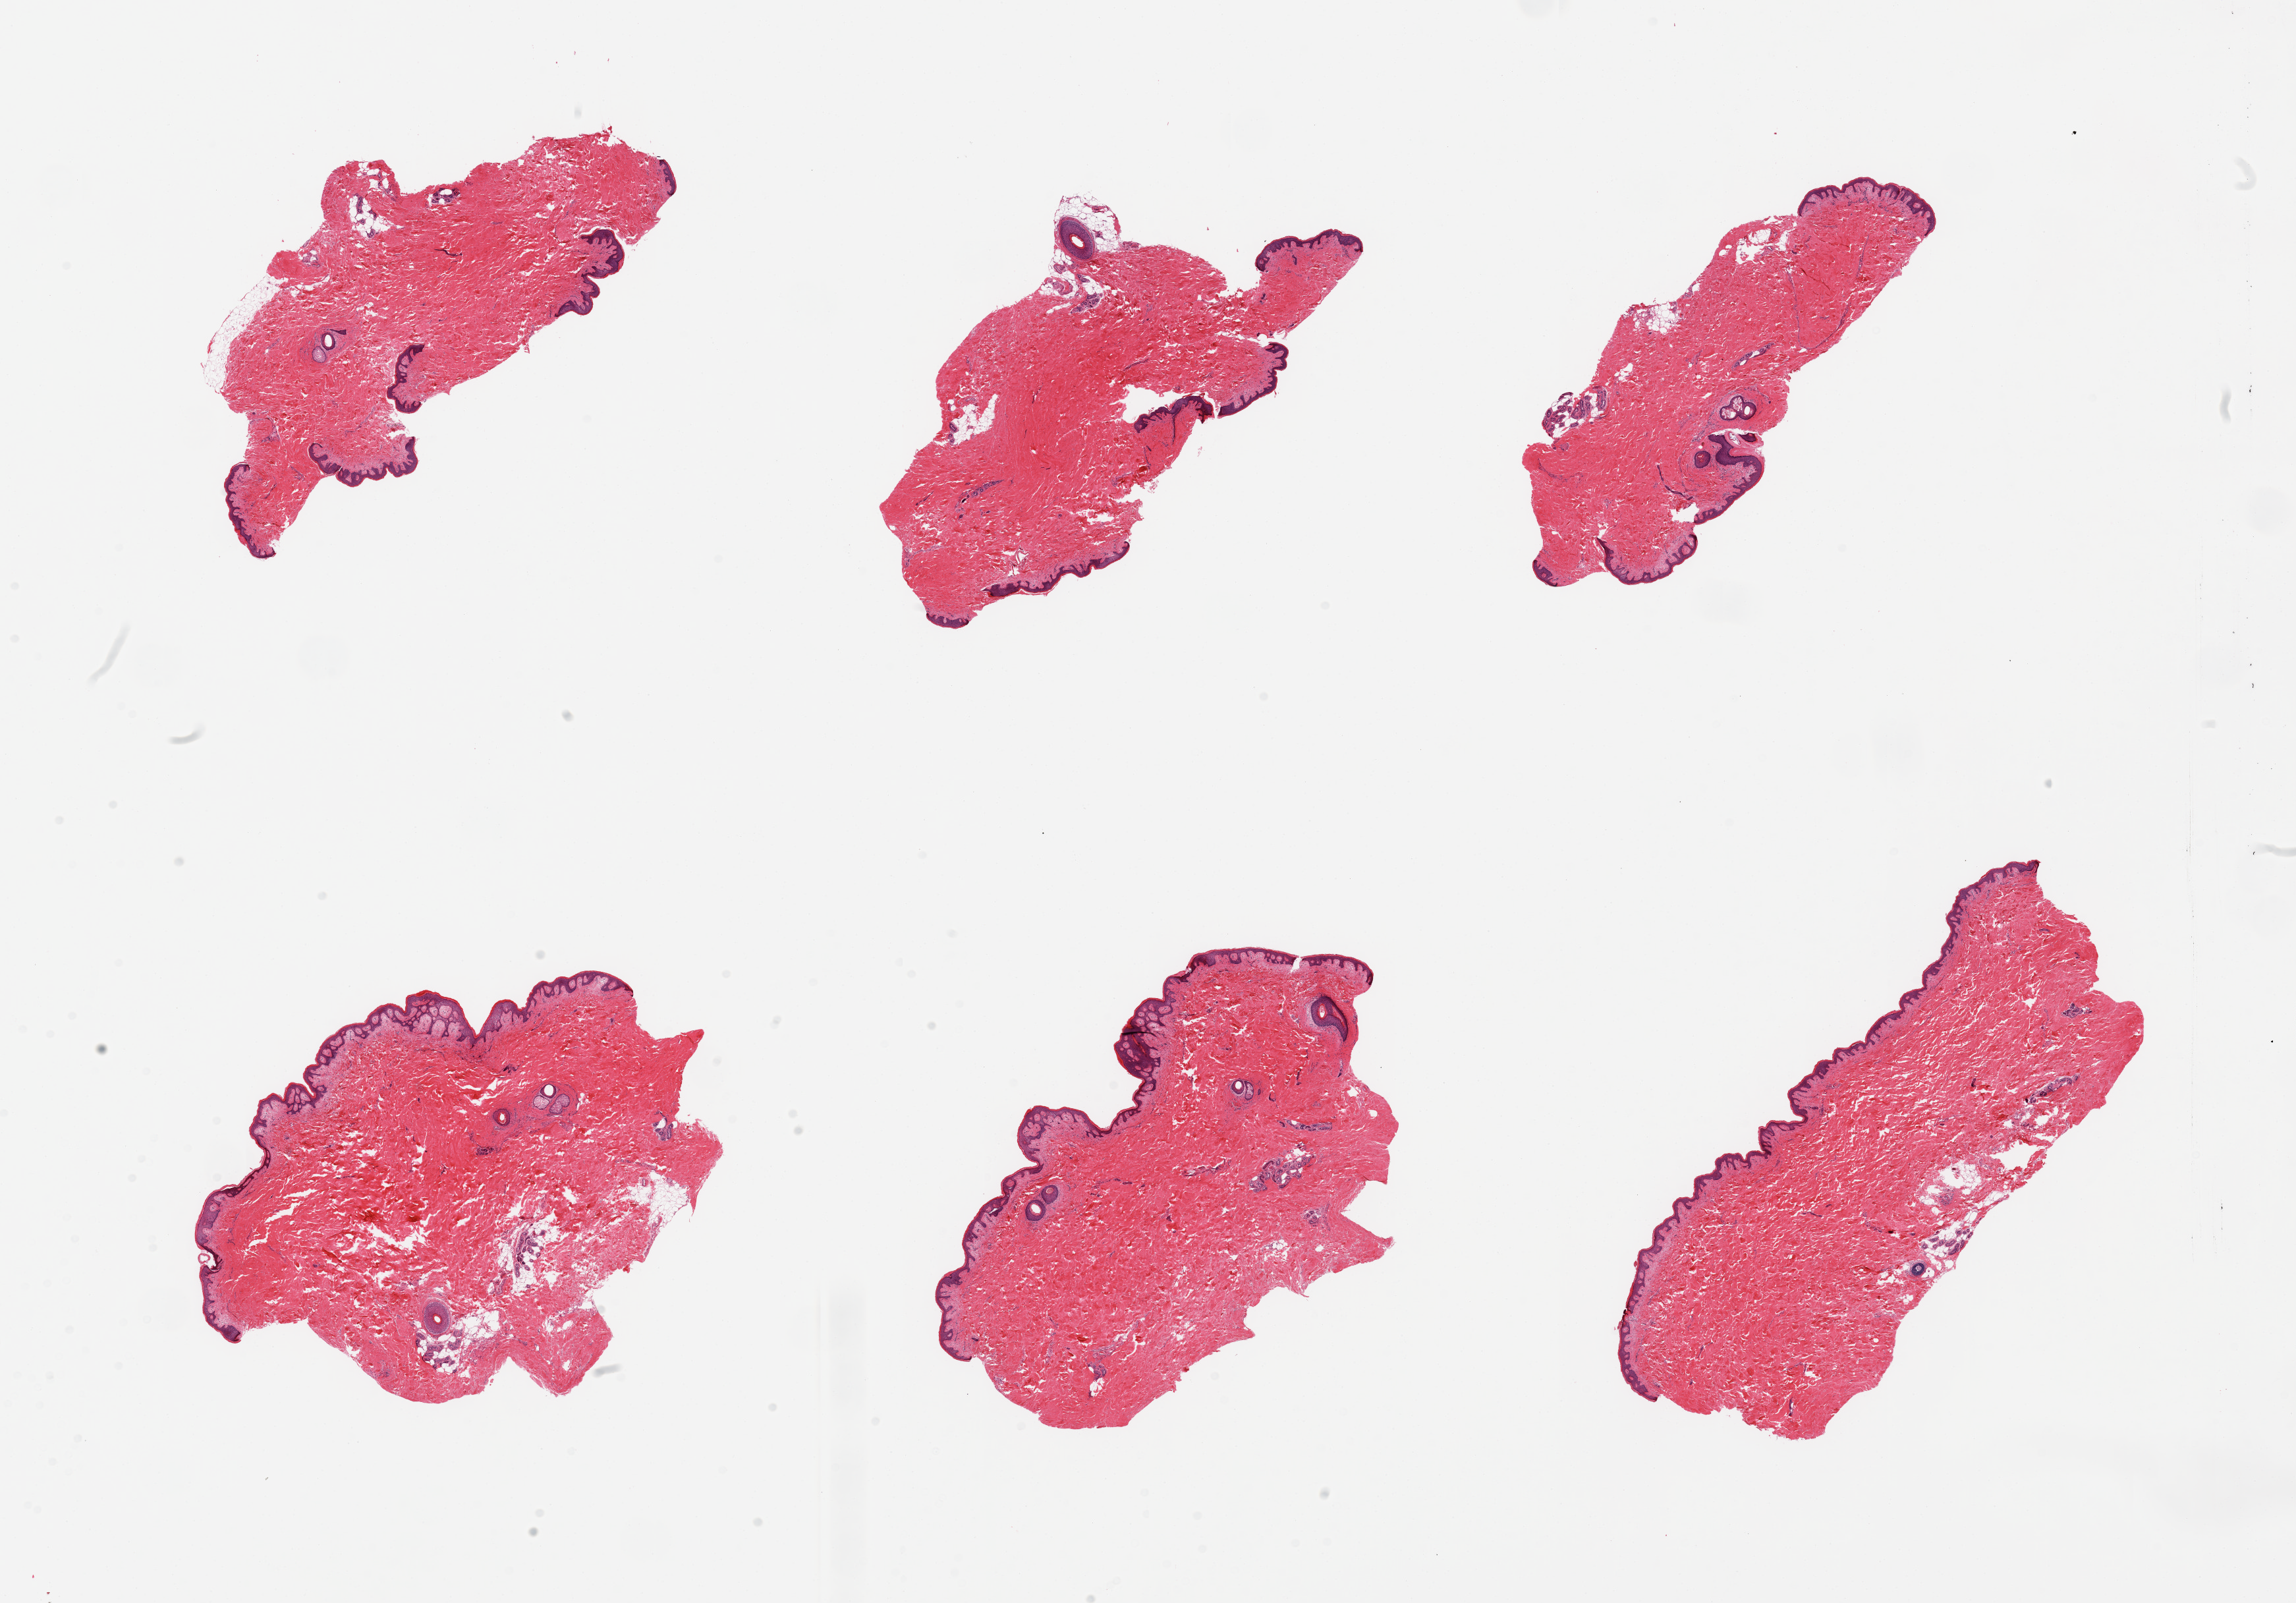
Haematoxylin and eosin whole-slide image — low-resolution overview of the scanned area, about 27.6 x 19.2 mm (slide scanned at 20x). PAXgene-fixed paraffin-embedded (PFPE) section. Section of skin of suprapubic region (target tissue). Tissue donor sample. Donor: male.
Pathologist's review note for this sample: 6 pieces; well trimmed; 5% dermal fat.